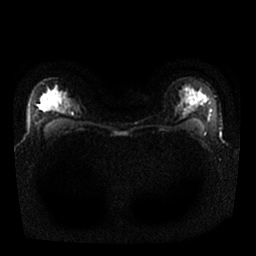
Breast MRI, one axial slice. Position 18 of 25 along the scan axis. Diffusion-weighted series; image 2 of 4 stored at this slice position (different b-values; order by instance number). 1.5 T. 4 mm slice thickness. 256 × 256 image matrix, field of view 340 × 340 mm. Female patient.
Outlined on this slice (manually delineated by an expert):
- tumour on diffusion-weighted imaging: bounding box (x1, y1, x2, y2) in pixels: (41, 100, 50, 109)